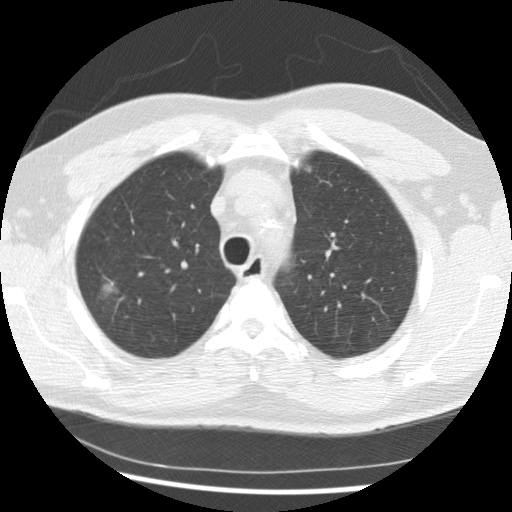
Chest CT (low-dose screening protocol), one axial image. First (baseline) screen. Lung window (W 1500 / L -600 HU). 2.5 mm slice thickness. Slice 61 of 265 in the series. 512 × 512 image matrix. Male participant, aged 56 years at enrolment. Current smoker at enrolment.
- Lesion marked by an expert reader, bounding box <75,267,131,316> (left, top, right, bottom; pixels).
- The exam's reader record, not a measurement of the box and not confirmed to be the same lesion: non-calcified nodule or mass ≥4 mm, right upper lobe, 19 × 15 mm, spiculated (stellate) margins, soft tissue attenuation.